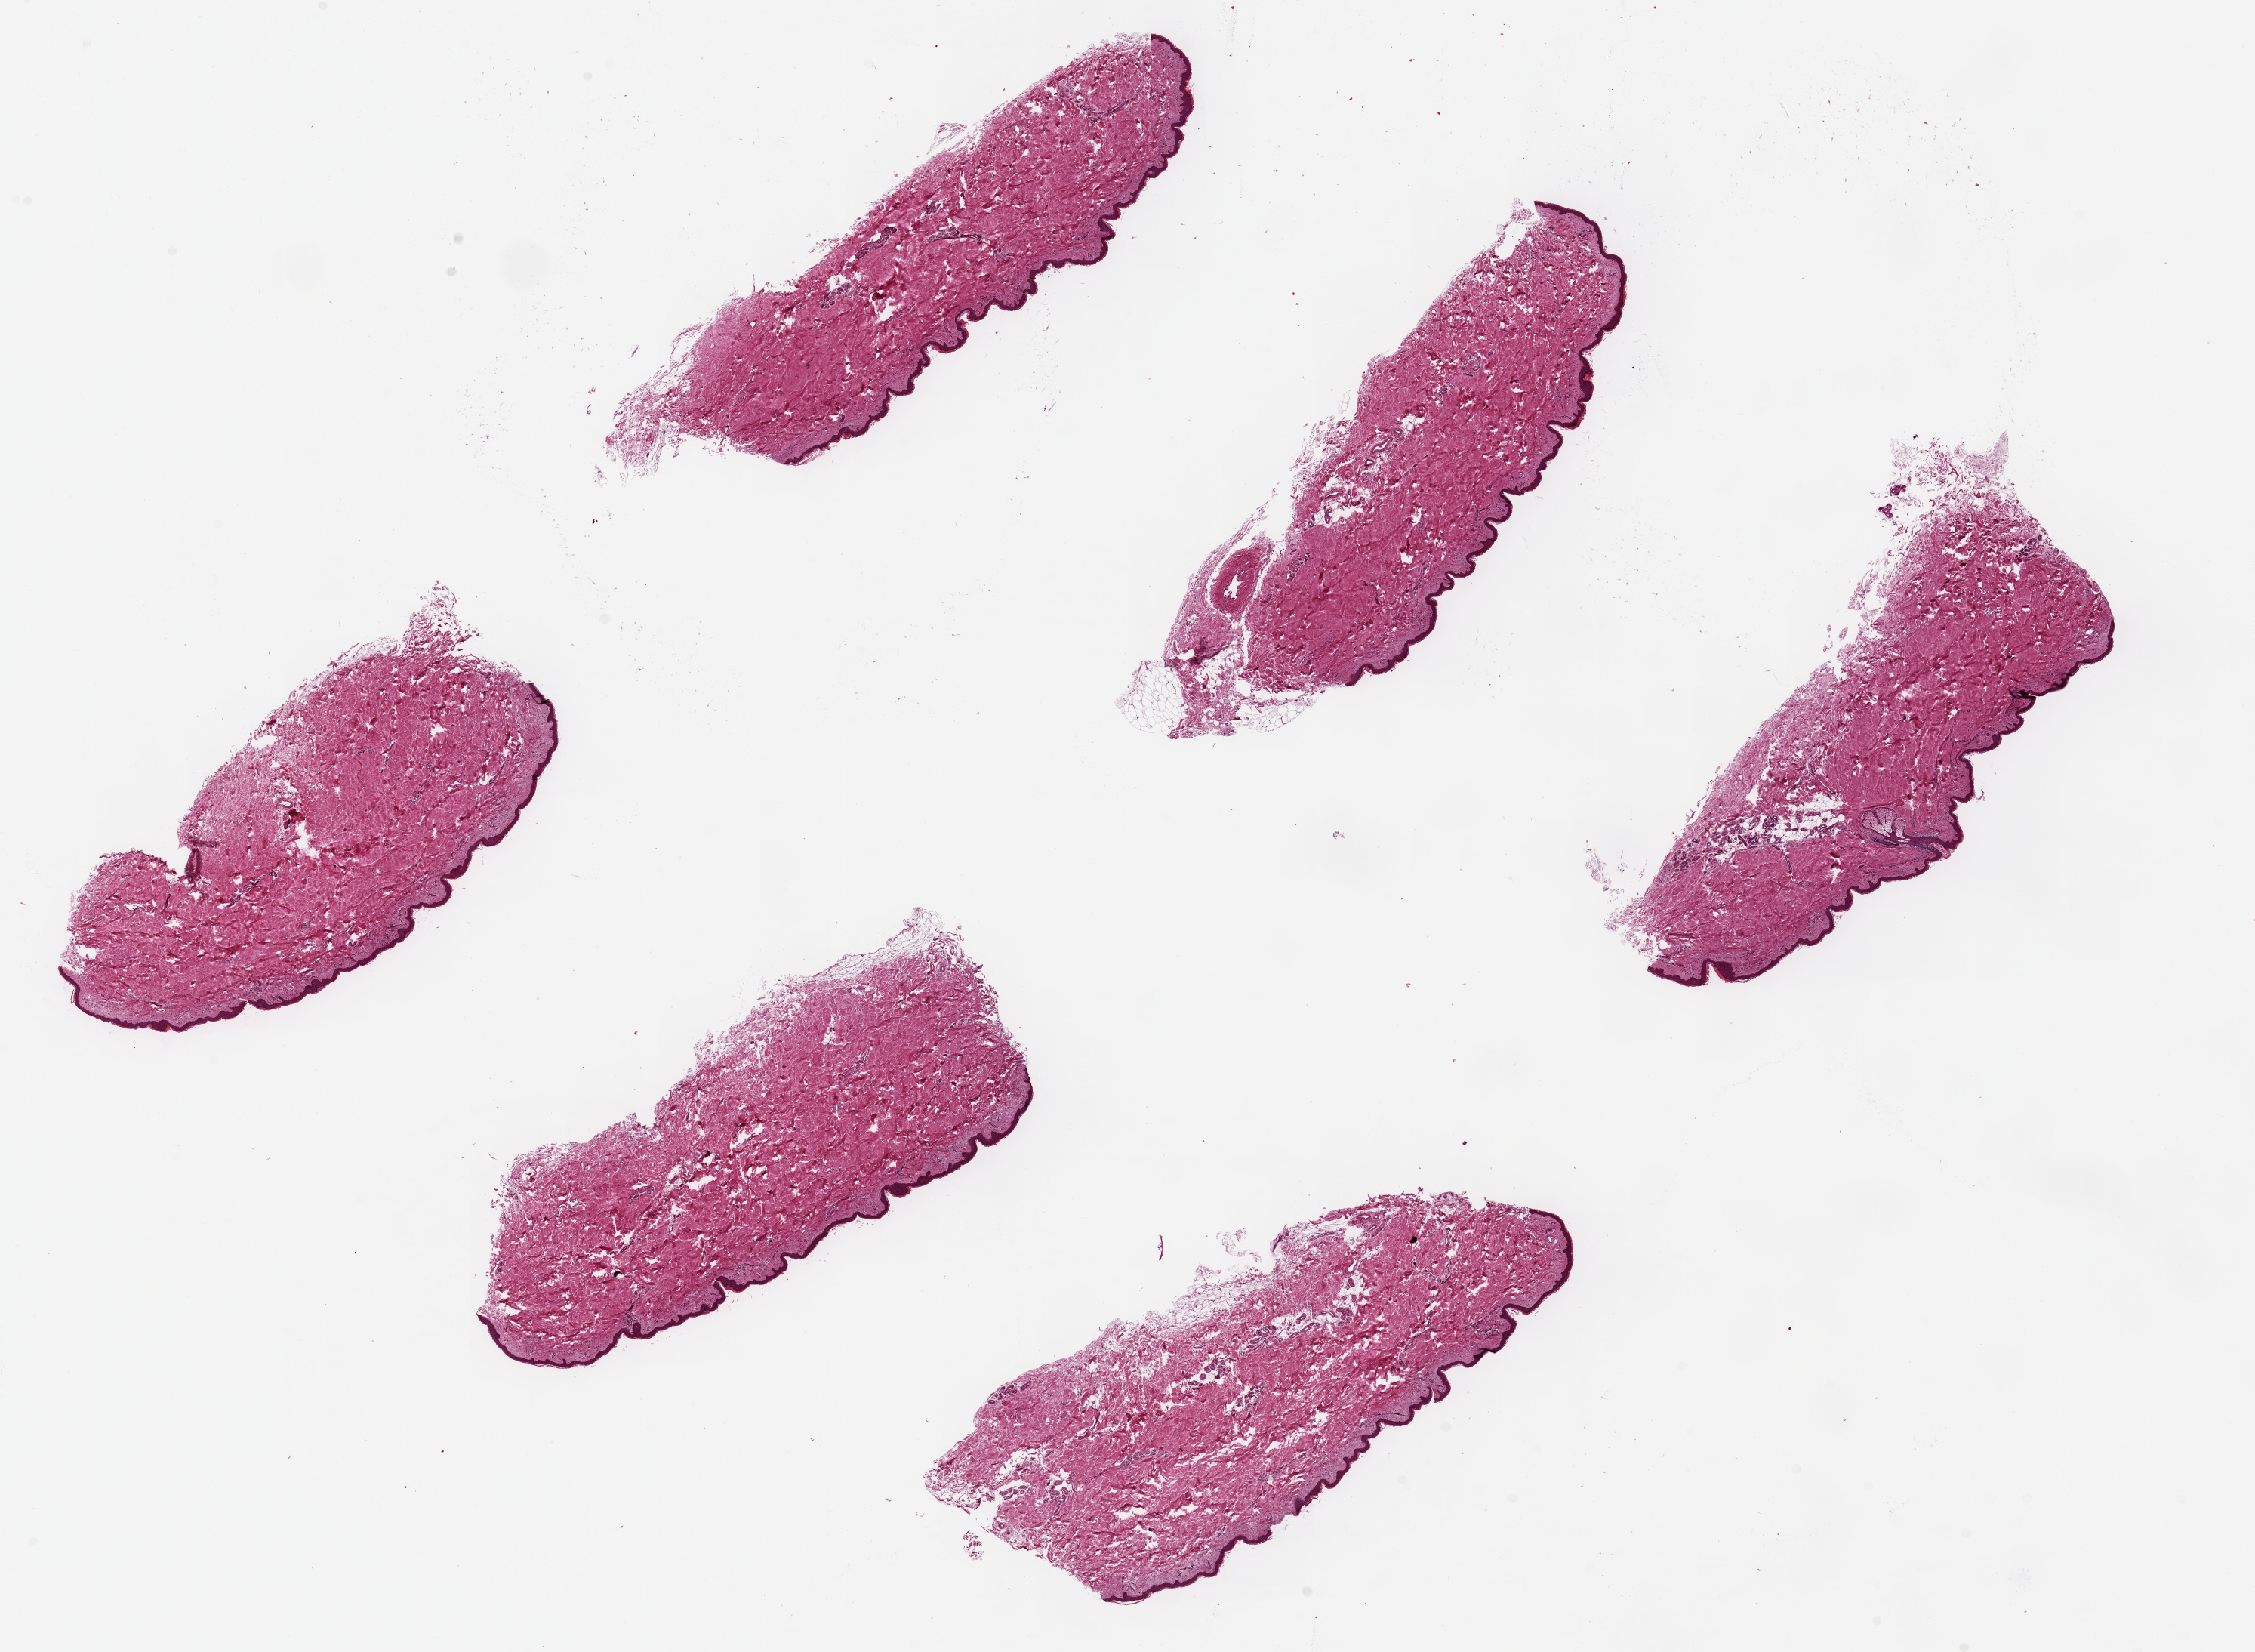
Whole-slide image, haematoxylin and eosin stain, brightfield — low-resolution overview of the scanned area, about 23.6 x 17.3 mm (acquisition: 20x scan), PAXgene-fixed paraffin-embedded (PFPE) section, sampled site (target tissue): skin of lower leg, donor tissue sample. Donor: male.
Pathologist's review note for this sample: 6 ~6.5x2.5mm pieces; squamous epithelium is ~1-2% of thickness.